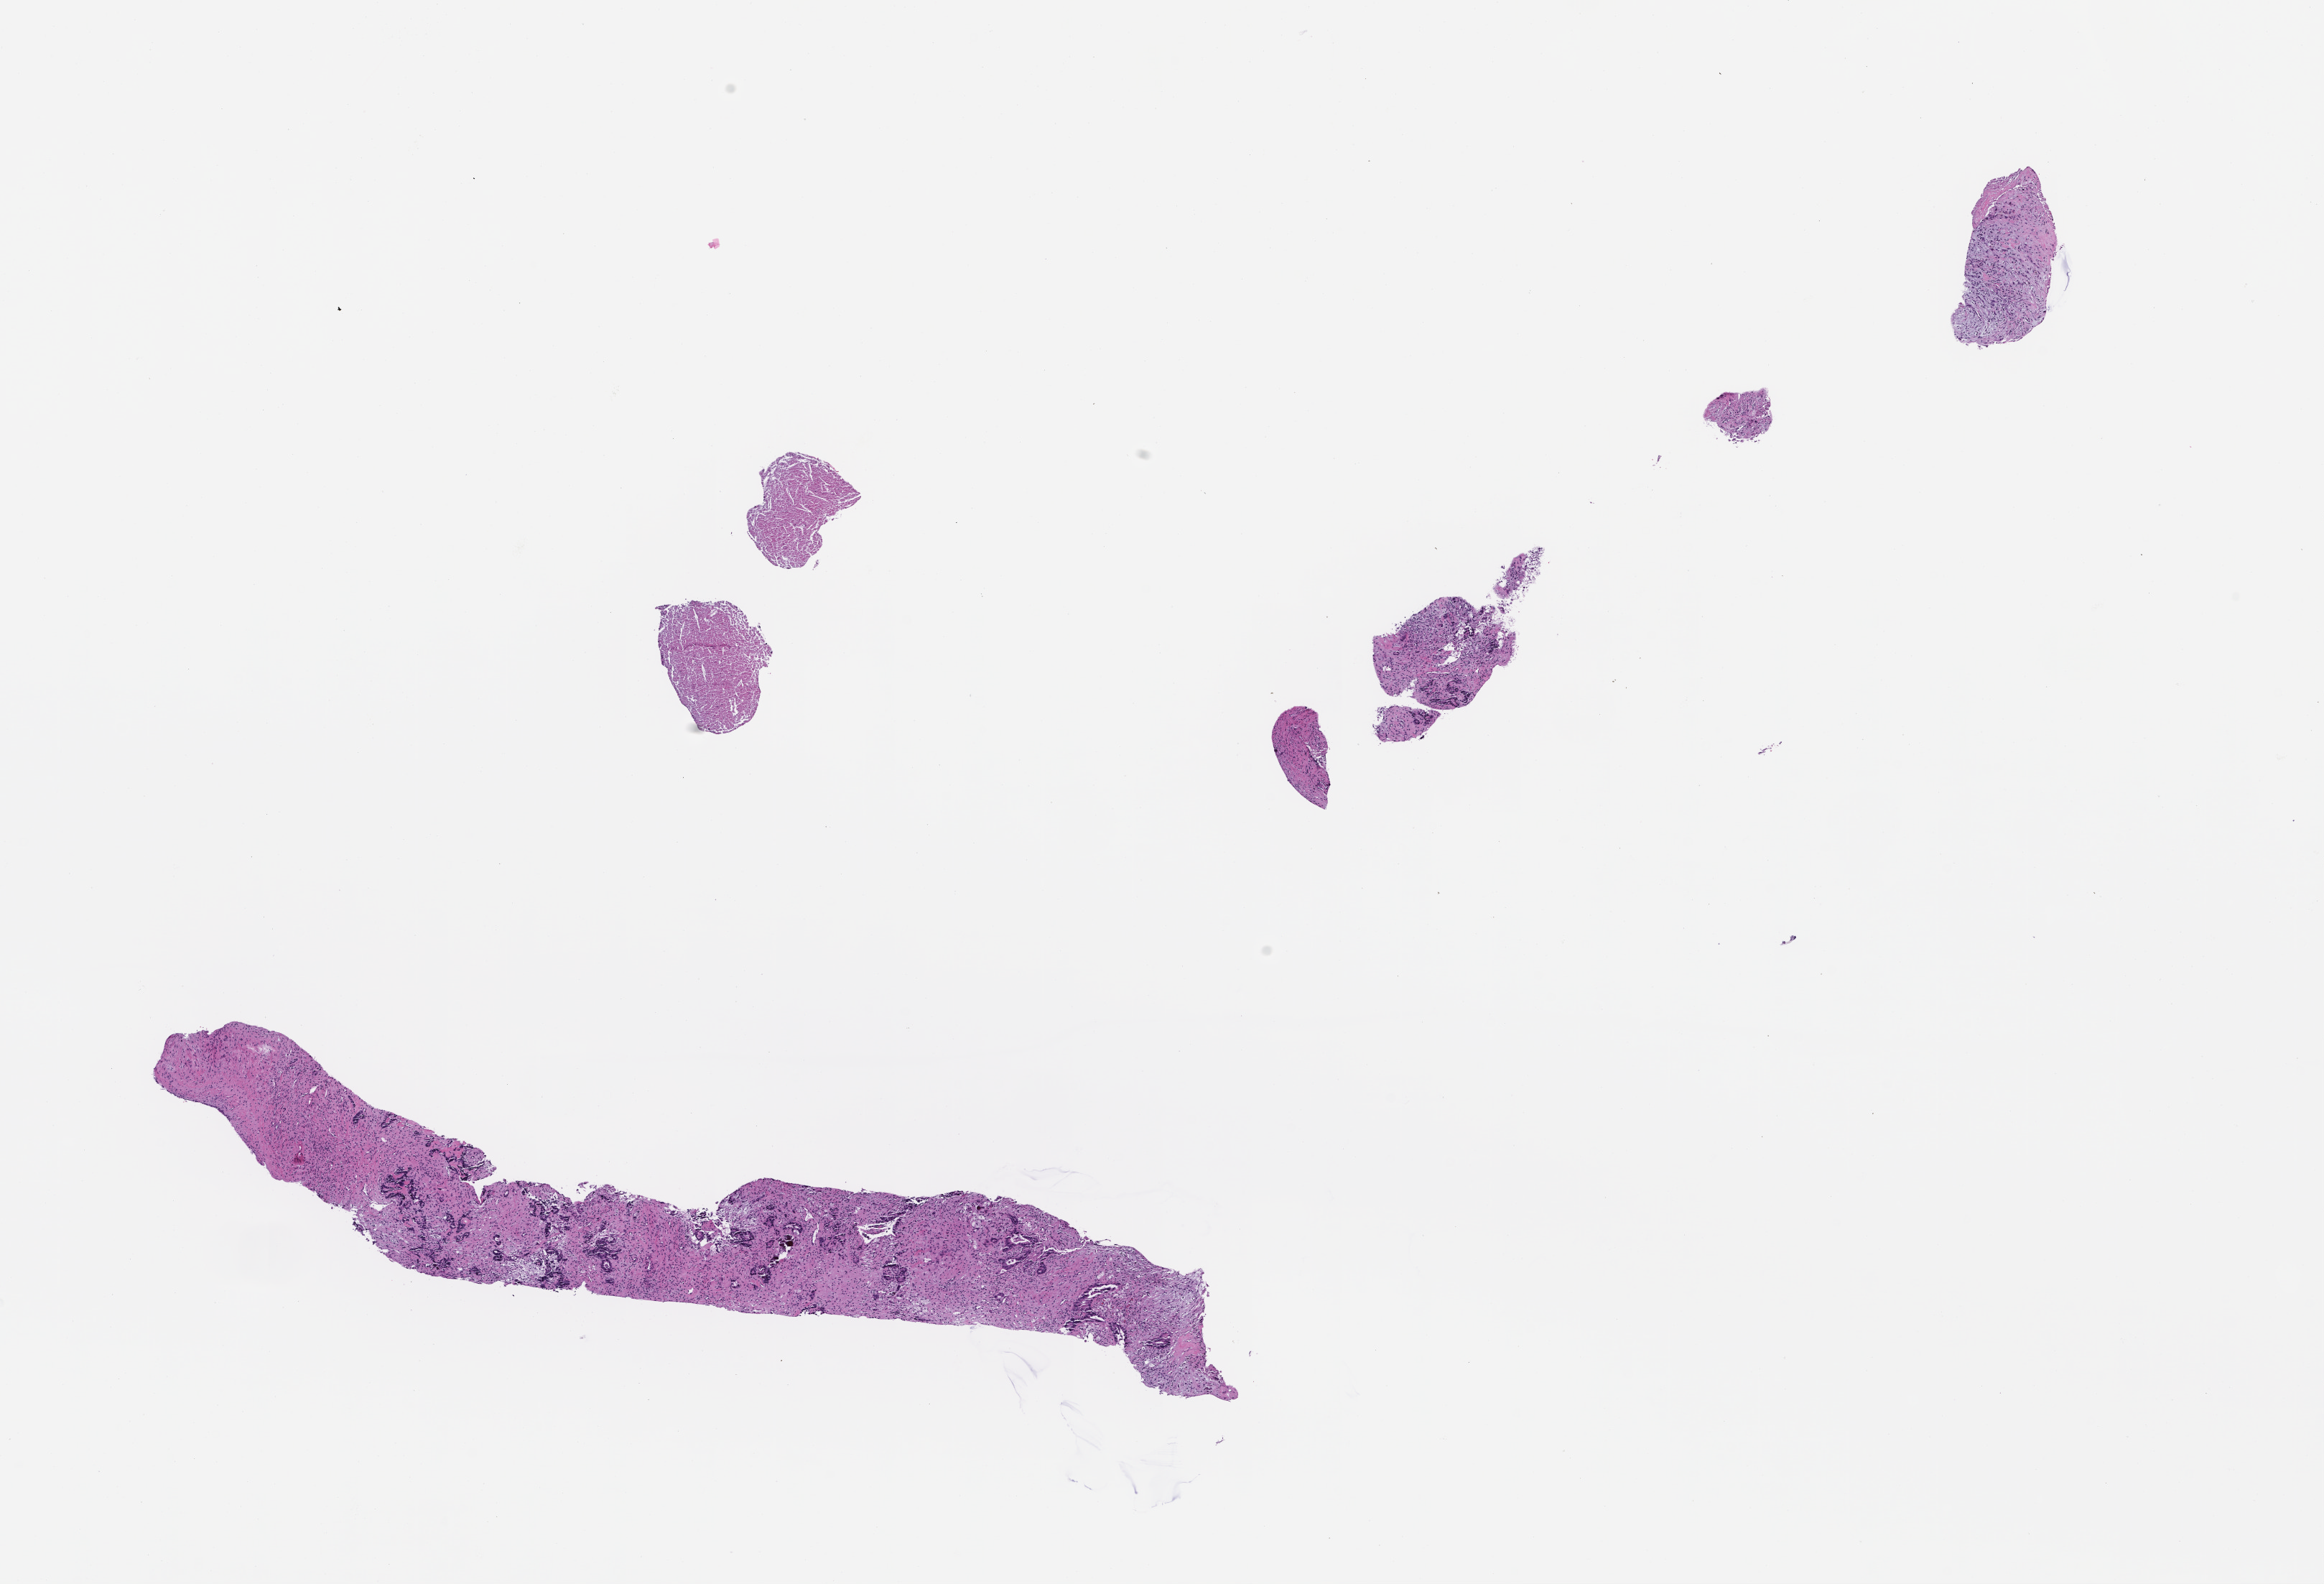
Whole-slide image, haematoxylin and eosin stain — shown as a low-resolution overview of the whole scanned area (about 13.1 x 8.9 mm), formalin-fixed paraffin-embedded section, specimen time point: collected at disease progression. Patient sex: male.
This section: metastasis (sampled organ not recorded). Patient diagnosis (primary): Colorectal Carcinoma.